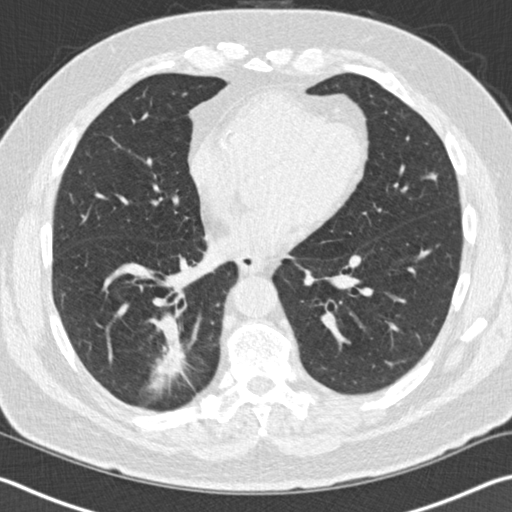
Low-dose screening chest CT, one axial slice. Slice 46 of 141 in the series (ordered by position). Reconstruction kernel B30f. 120 kVp. Lung window (W 1500 / L -600 HU). 2 mm slice thickness. 512 × 512 image matrix, field of view 344 × 344 mm.
Annotated regions visible in this slice (outlined manually by an expert reader):
- lesion 1 (tumor, lower lobe of right lung): bounding box <154,318,188,381> (left, top, right, bottom; pixels)